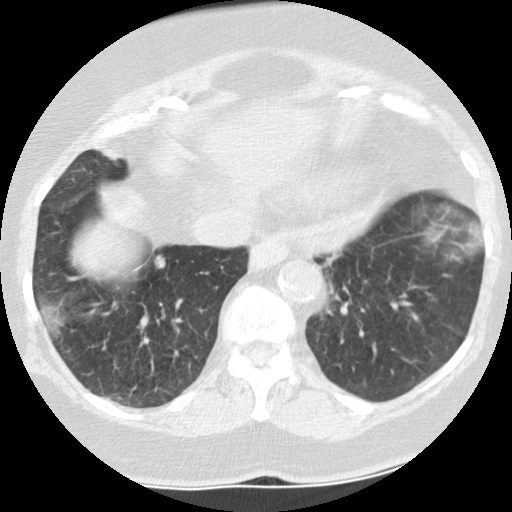
Low-dose screening chest CT, one axial slice; position 39 of 157 along the scan axis; 120 kVp; lung window (W 1500 / L -600 HU); 512 × 512 image matrix, field of view 304 × 304 mm.
Outlined on this slice (manually delineated by an expert):
- lesion 1 (tumor, lower lobe of right lung): bounding box [x1, y1, x2, y2] px = [156, 256, 165, 268]